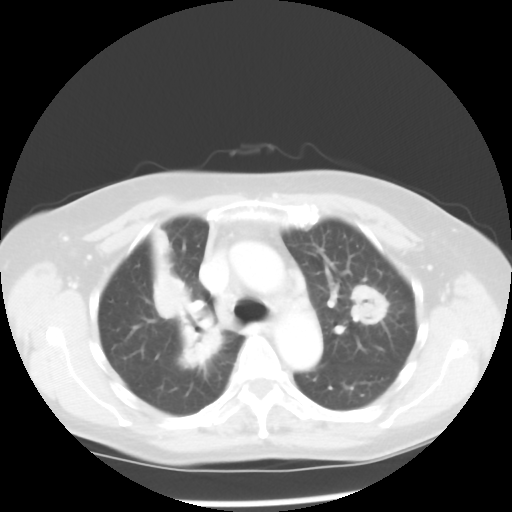
Chest CT, one axial slice; position 36 of 52 along the scan axis; reconstruction kernel STANDARD; 100 kVp; lung window (W 1500 / L -600 HU); 5 mm slice thickness; 512 × 512 image matrix, field of view 328 × 328 mm. Female patient, age 60 years. Case-level facts recorded for this patient, not image findings: clinical TNM (as recorded): T2 N1 M1a.
Outlined on this slice (rectangle marked by the reading radiologist):
- lung tumour (recorded histology: adenocarcinoma): bounding box [x1, y1, x2, y2] px = [143, 223, 231, 372]